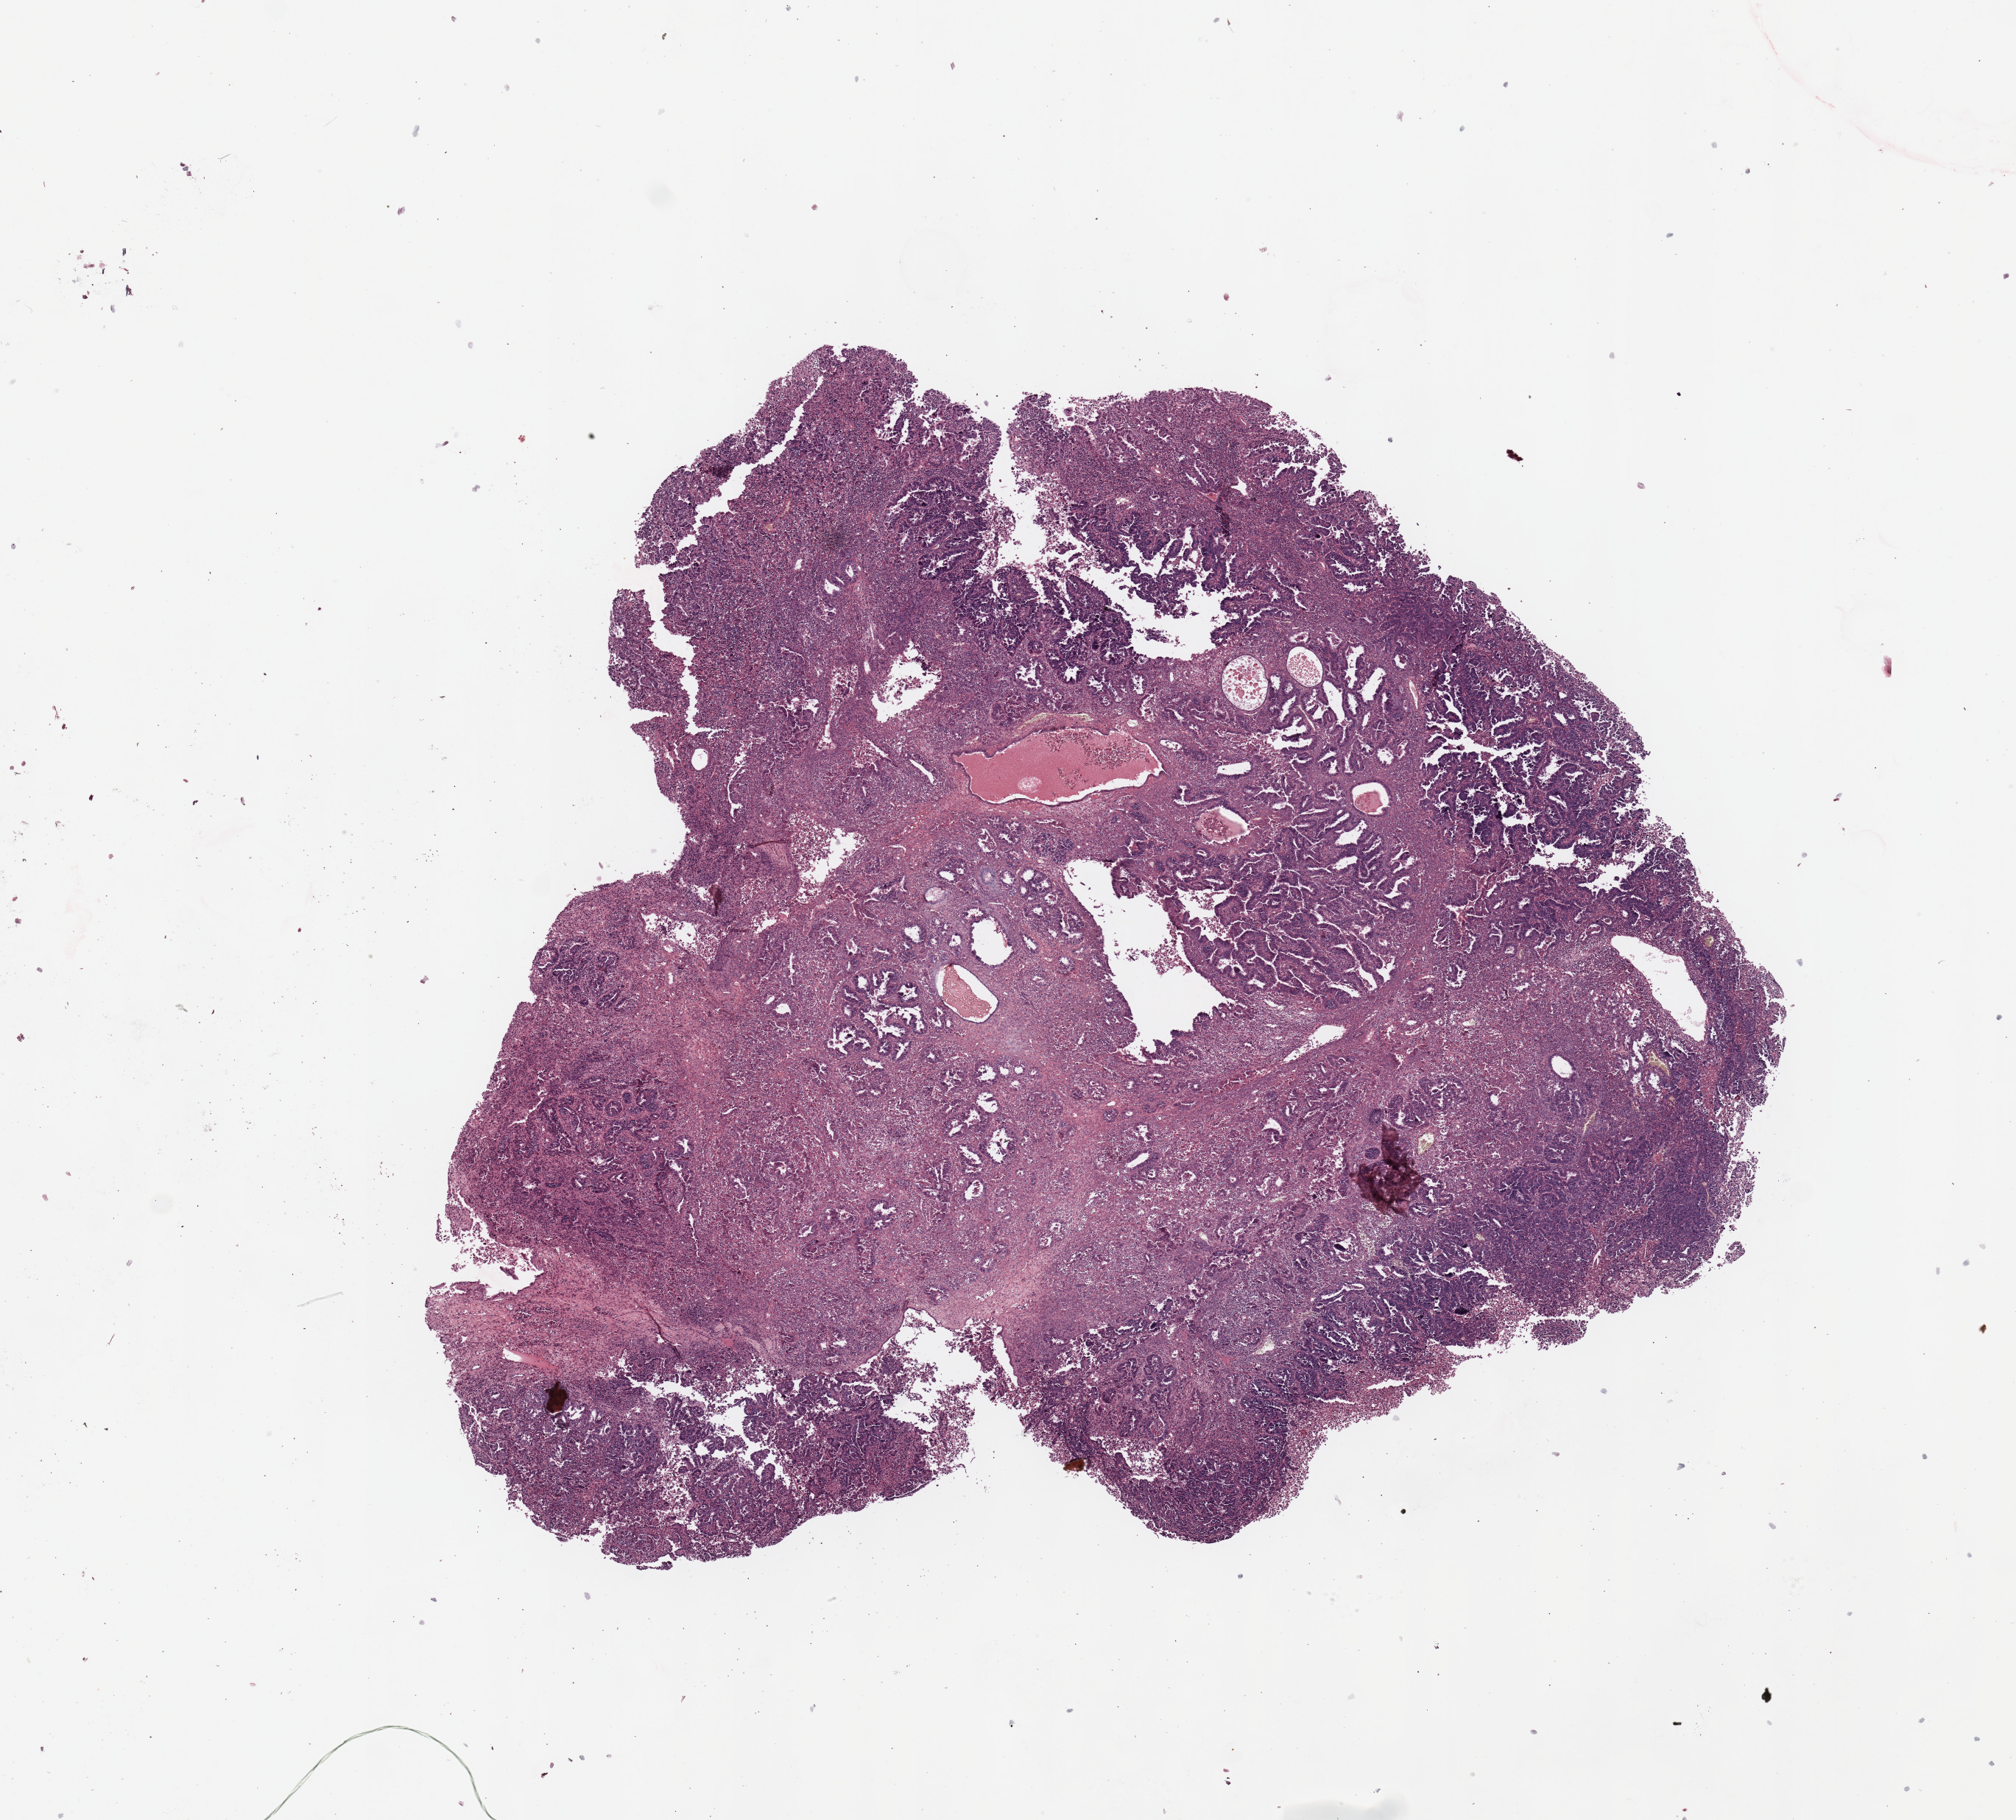
Hematoxylin and eosin (H&E) stained whole-slide image, shown as a low-resolution overview of the whole scanned area (about 10.8 x 9.8 mm, acquisition: 20x scan); tumour tissue sample, uterus. Patient: female, age 74 years. Histologic grade: G3 (poorly differentiated).
* AJCC pathologic stage: II
* diagnosis: Endometrioid adenocarcinoma, NOS